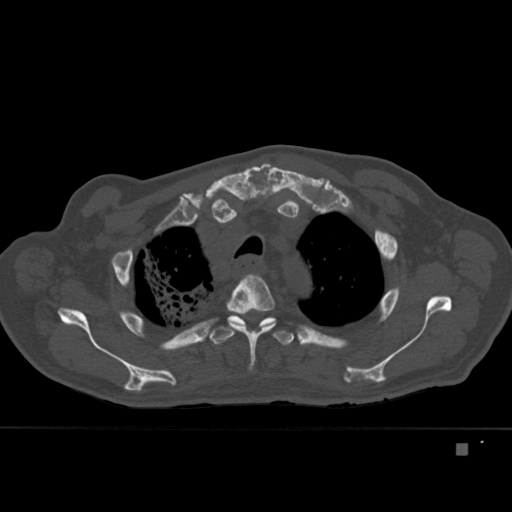
CT including the spine, one axial slice; position 330 of 451 along the scan axis; bone window (W 1800 / L 400 HU); 1.5 mm slice thickness; 512 × 512 image matrix, field of view 378 × 378 mm. Male patient, age 75 years. From the clinical record (not read from this slice): primary cancer: prostate.
Annotated regions visible in this slice (semi-automatically segmented with operator editing):
- T3 vertebra: bounding box <226,274,277,370> (left, top, right, bottom; pixels)
- T4 vertebra: <207,315,294,345>